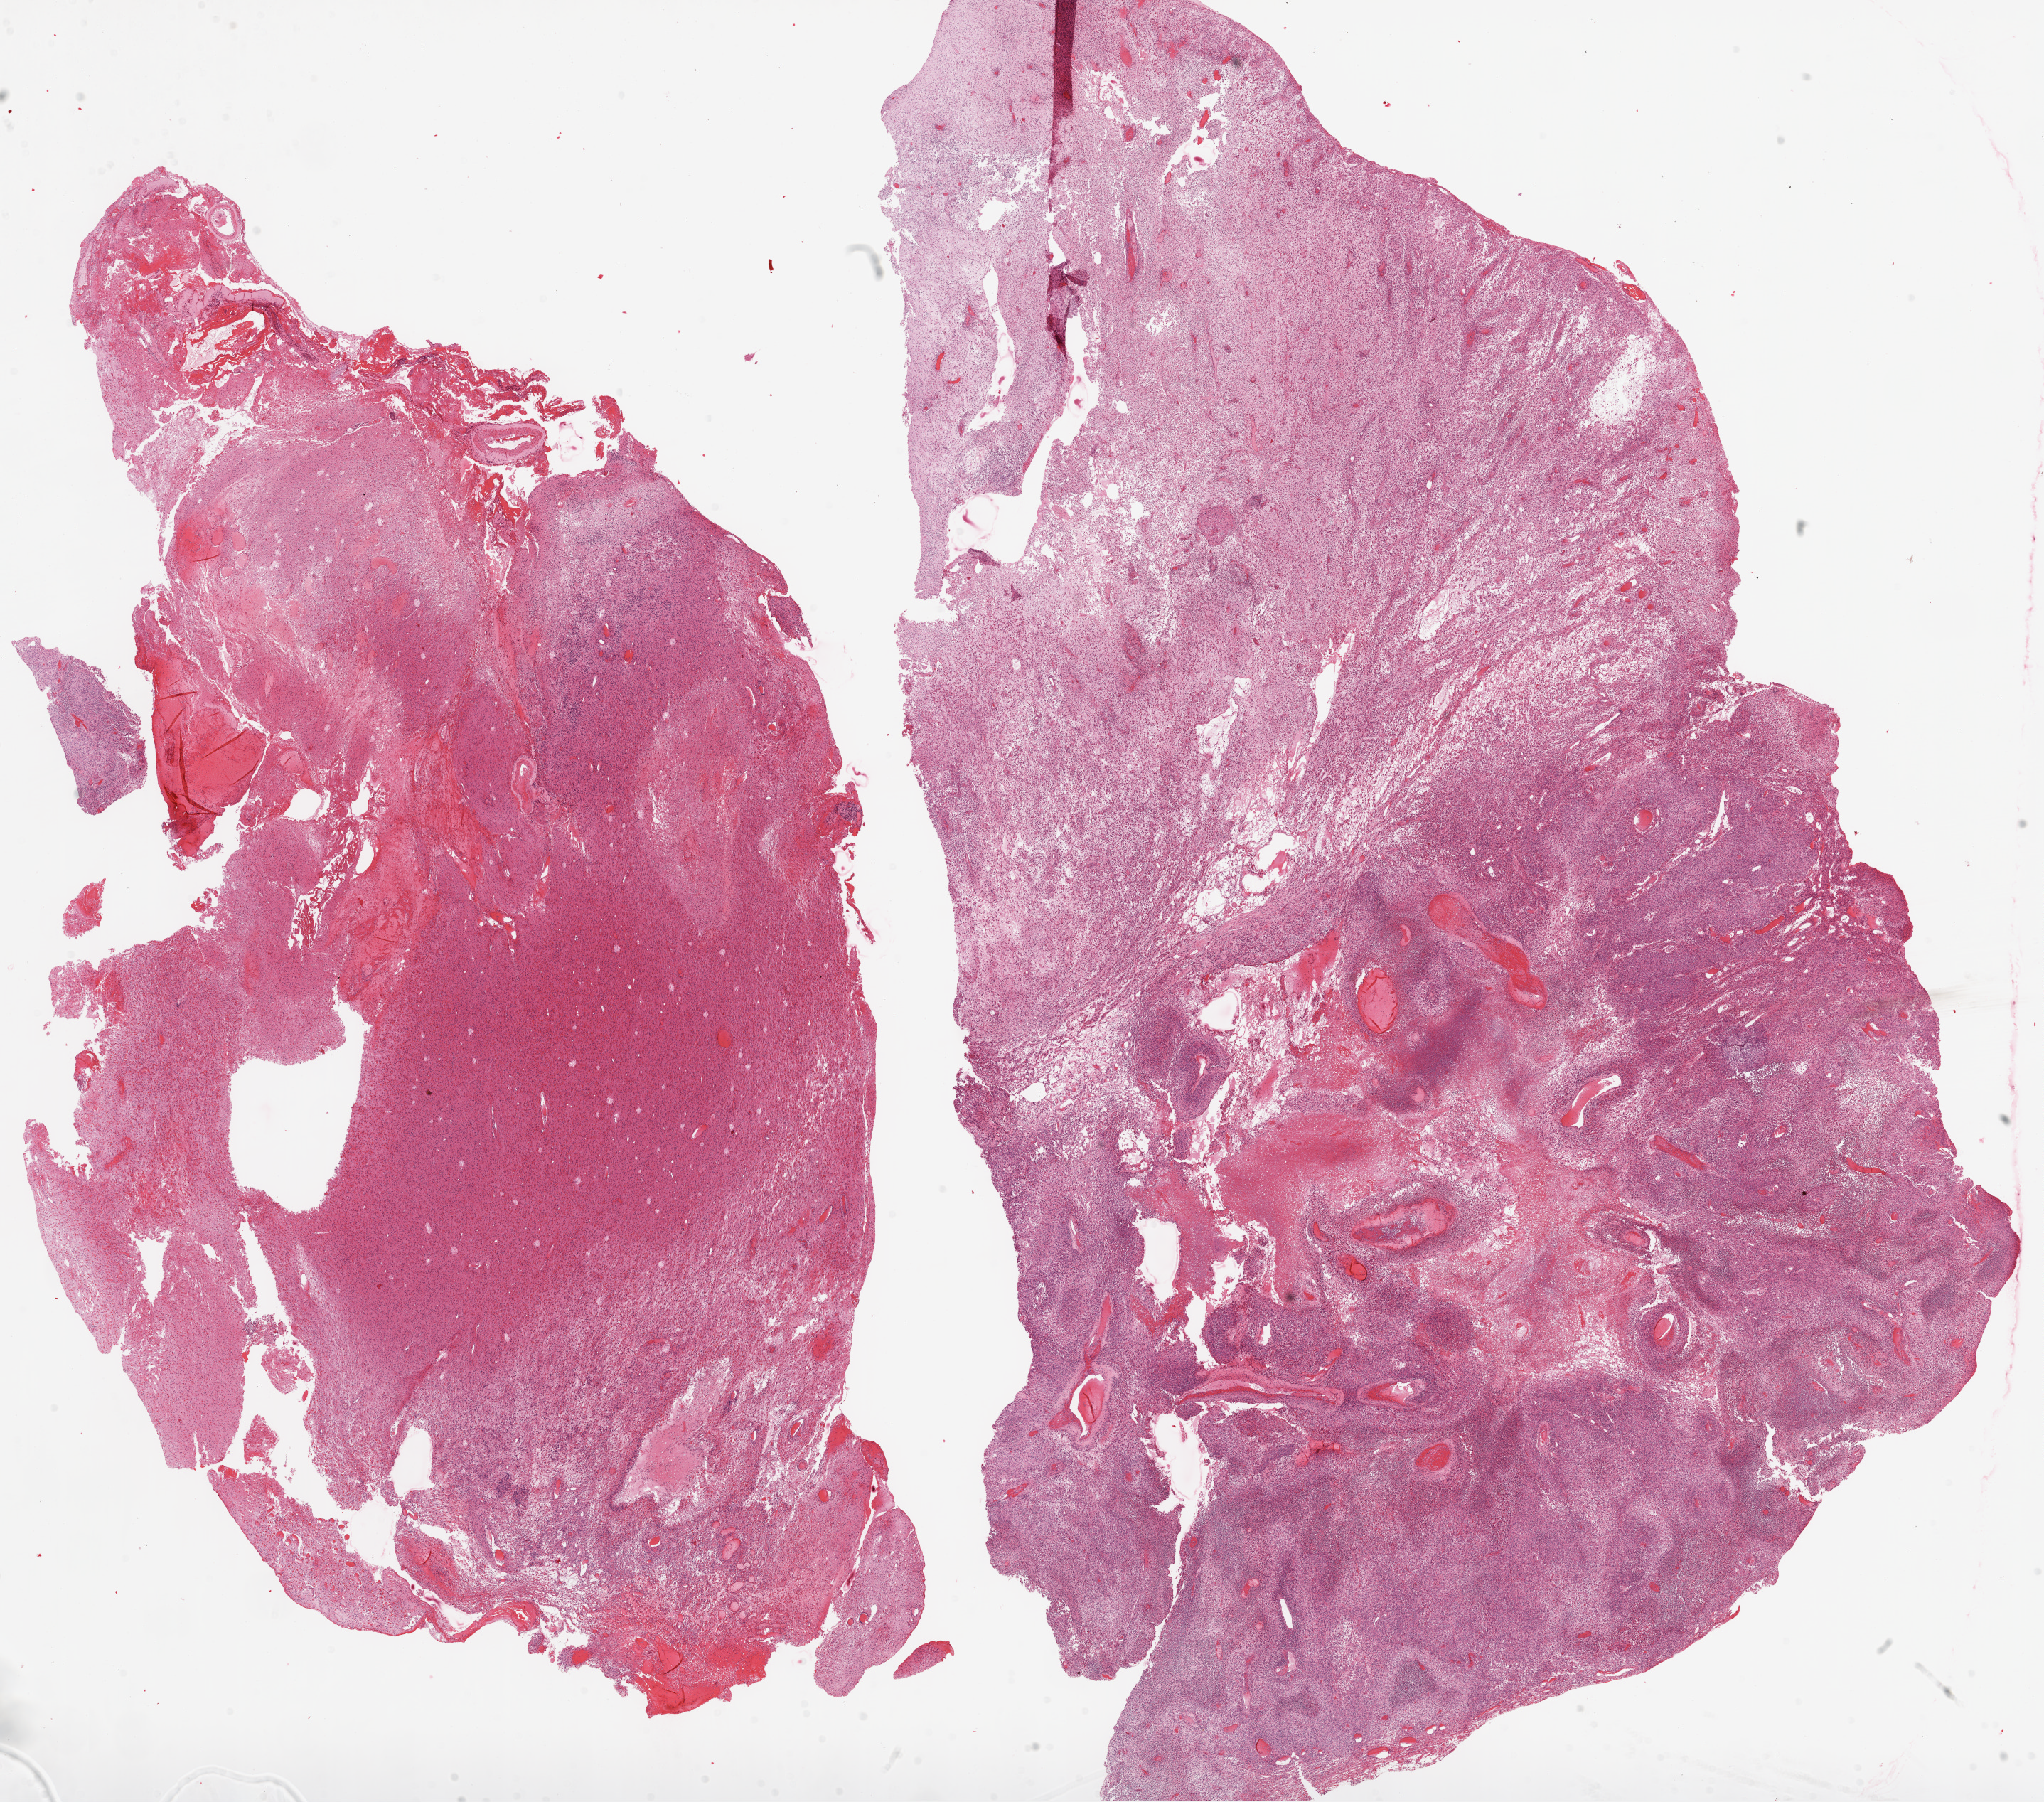
Hematoxylin and eosin (H&E) stained whole-slide image — a low-resolution overview of the entire scanned area, about 23.1 x 20.3 mm (slide scanned at 20x); FFPE section; sample: primary tumour, brain. Patient: female, age at initial diagnosis 59 years.
Histologic diagnosis: Glioblastoma.